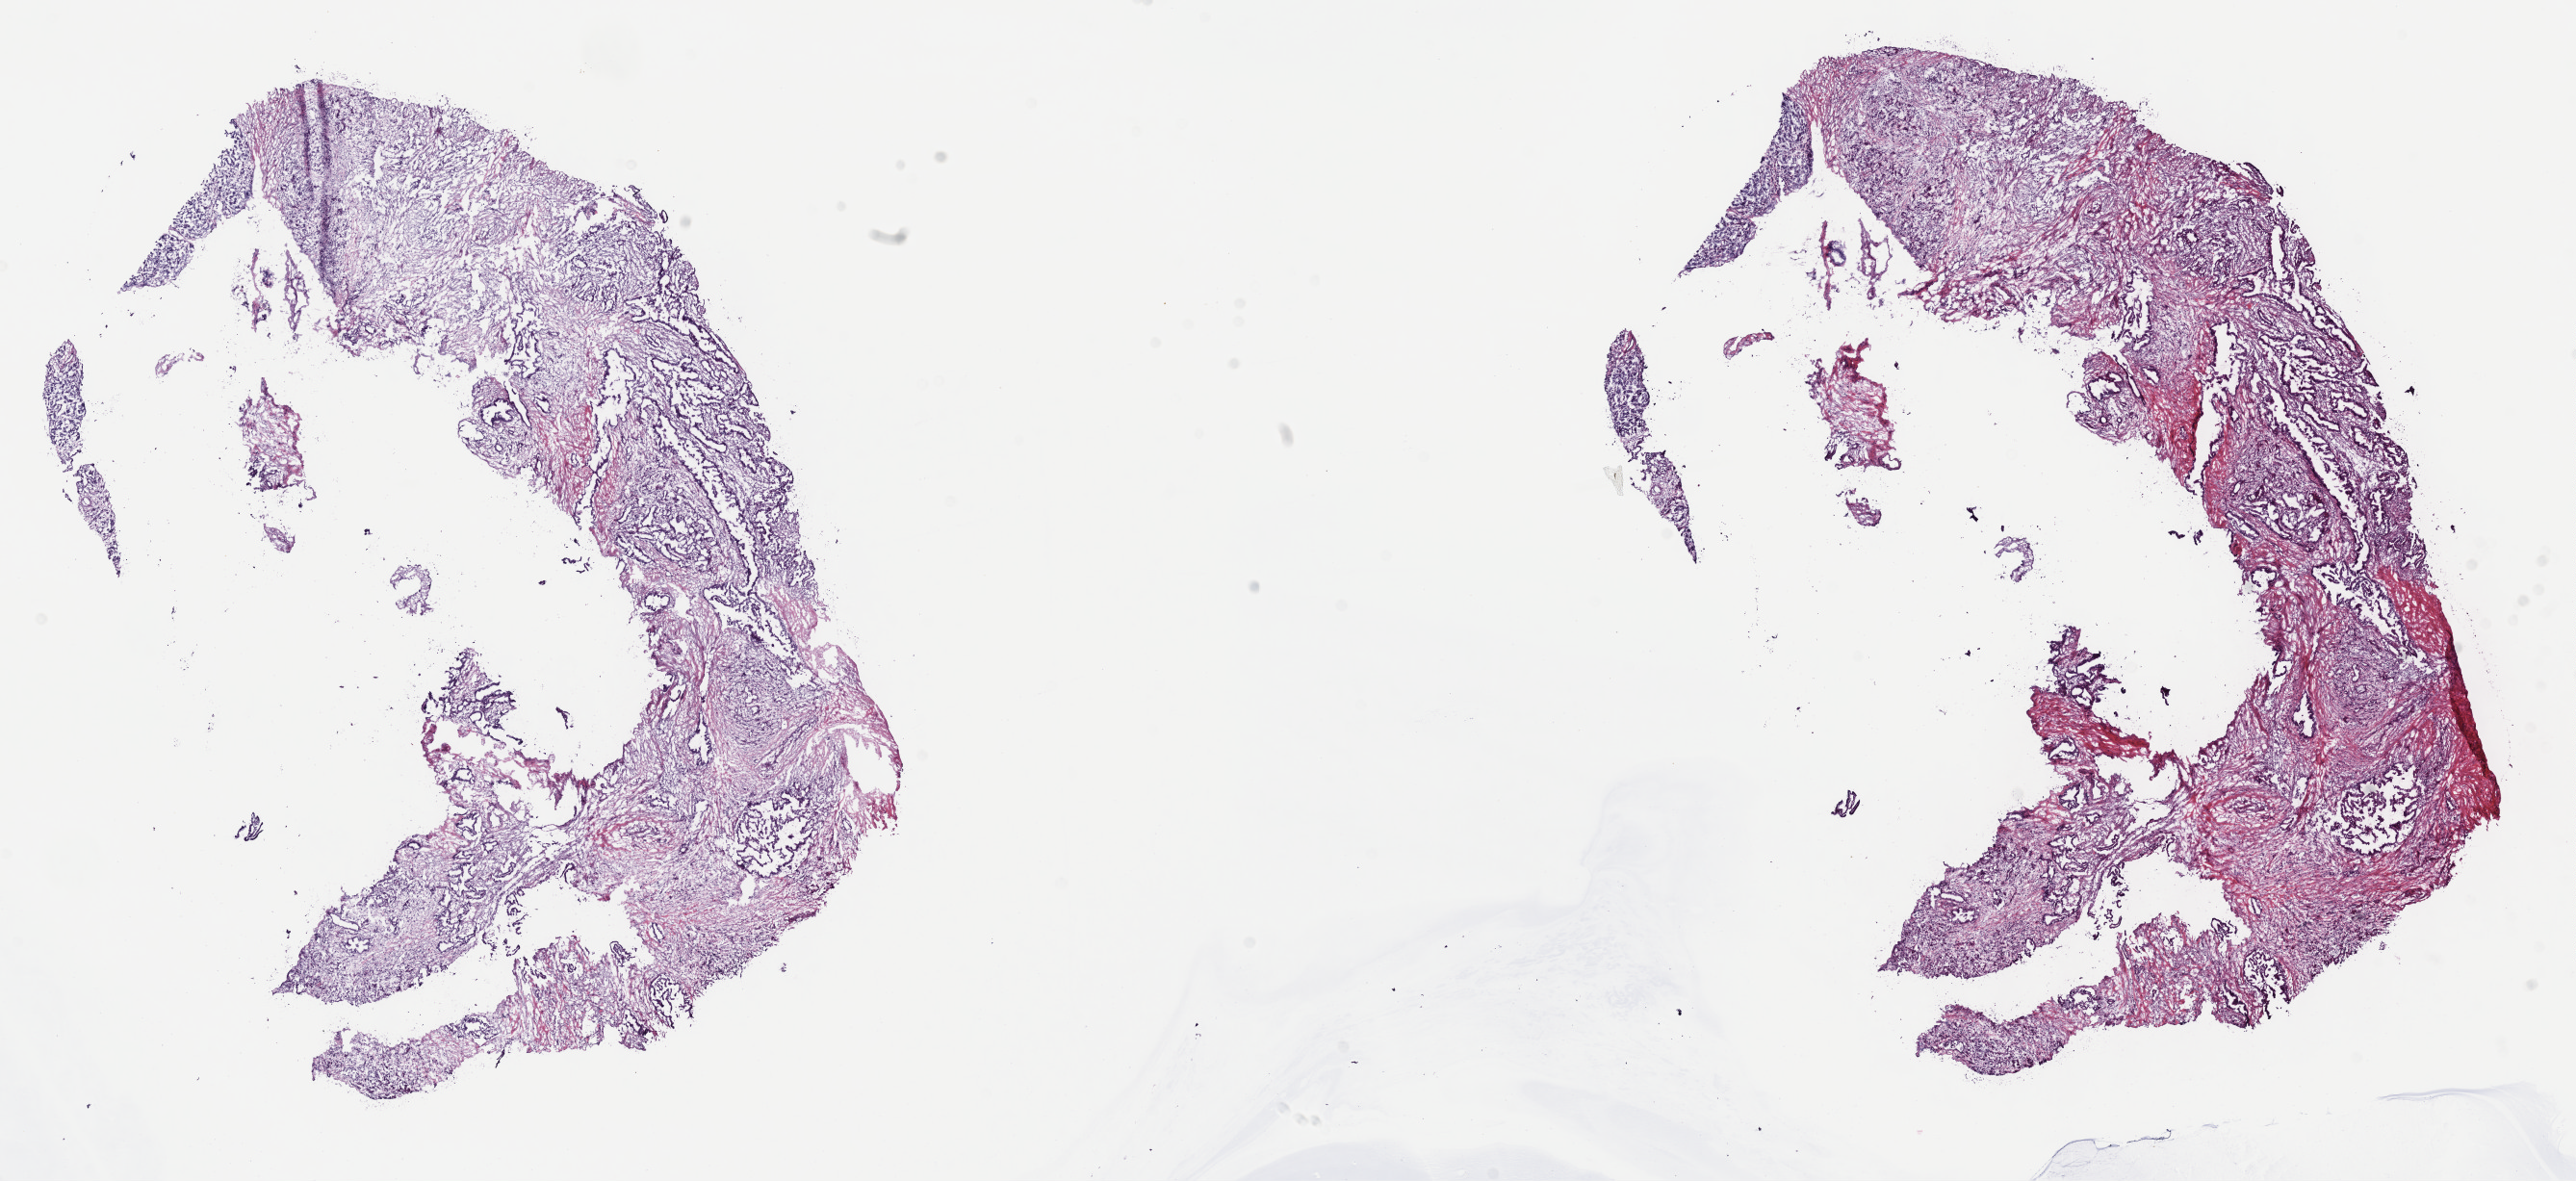
H&E whole-slide image — a low-resolution overview of the entire scanned area, about 21.6 x 9.9 mm. Frozen section from the top of the tissue portion. Sample: primary tumour, pancreas. Female patient; age at initial diagnosis 65 years. Histologic grade: G2 (moderately differentiated). Composition of this section per pathologist review: tumour cells 100%, tumour nuclei 60%, normal cells 0%, stromal cells 0%, necrosis 0%. Infiltration values recorded for this section: lymphocyte infiltration 3%, monocyte infiltration 0%, neutrophil infiltration 0%.
TNM: T3 N1 MX. Lymph nodes positive (case pathology): 1 of 23 examined. AJCC pathologic stage: IIB (7th edition). Pathologic diagnosis: Infiltrating duct carcinoma, NOS.